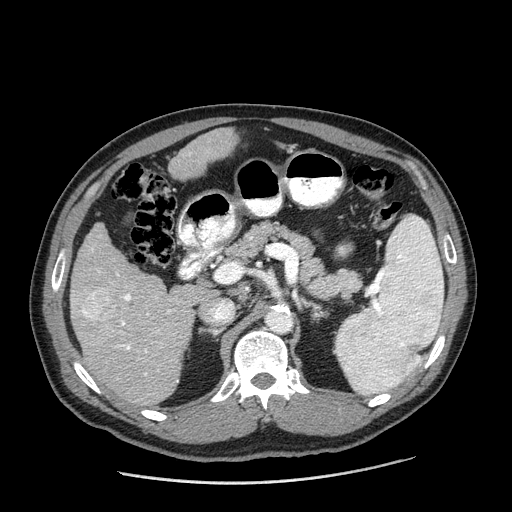
Contrast-enhanced abdominal CT (liver protocol), one axial slice. Slice 97 of 198 in the series (ordered by position). Reconstruction kernel STANDARD. One of 2 acquisitions stored at this slice position. Soft-tissue window (W 400 / L 40 HU). 2.5 mm slice thickness. 512 × 512 image matrix, field of view 400 × 400 mm. From the clinical record (not read from this slice): diagnosis: hepatocellular carcinoma (patient treated with transarterial chemoembolisation; whether this scan precedes or follows treatment is not stated here); TNM stage (as recorded): Stage-II; Child-Pugh class: A; tumour differentiation: moderately differentiated; tumour nodularity: multinodular.
Annotated regions visible in this slice (semi-automatic segmentation, software-assisted and operator-edited):
- liver parenchyma outside the tumour (the mass and vessels are separate outlines, so this box may not span the whole liver): box from (x=70, y=128) to (x=236, y=406) px
- mass: (x=79, y=287)–(x=118, y=321)
- liver vessels: (x=98, y=270)–(x=171, y=376)